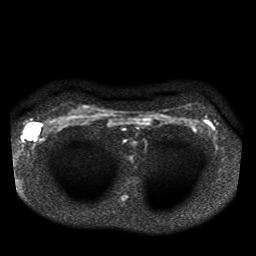
Breast MRI, one axial slice; slice 31 of 41 in the series (ordered by position); diffusion-weighted series; image 2 of 4 stored at this slice position (different b-values; order by instance number); 1.5 T; 5 mm slice thickness; 256 × 256 image matrix. Female patient.
Structures marked on this image (outlined manually by an expert reader):
- tumour on diffusion-weighted imaging: bounding box (x1, y1, x2, y2) in pixels: (23, 122, 41, 140)